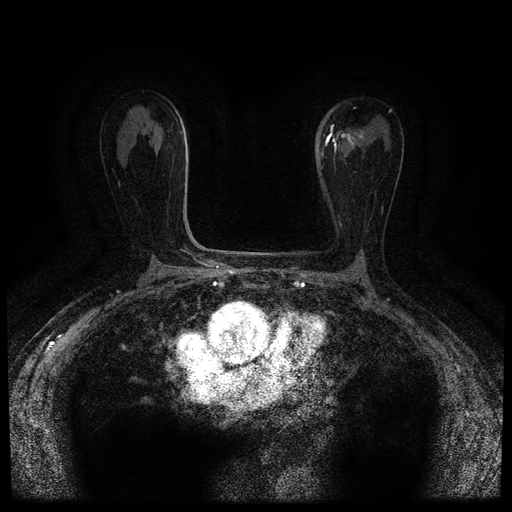
Breast MRI (dynamic contrast-enhanced, multi-phase), one axial slice; slice 47 of 116 in the series (ordered by position); dynamic contrast-enhanced series, time point 2 of 5 at this slice position (early post-contrast); 1.5 T; TE 2.7 ms, TR 5.4 ms; 512 × 512 image matrix, field of view 320 × 320 mm. Patient: female, 80 years.
Annotated regions visible in this slice (semi-automatically segmented with operator editing):
- breast lesion (labelled 'tumour' in the annotation; benign lesions carry a separate 'benign' label): bounding box <332,131,364,153> (left, top, right, bottom; pixels)